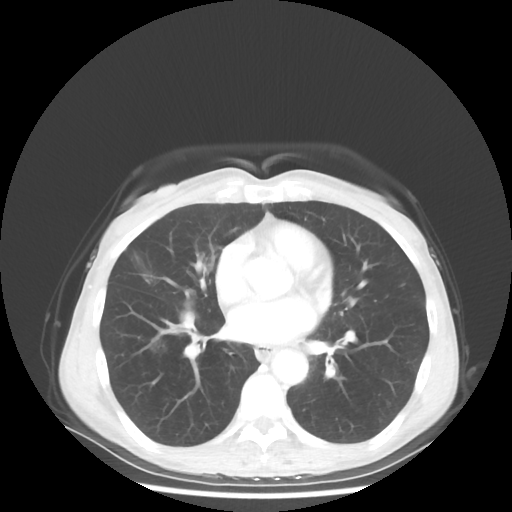
Chest CT, one axial slice. Position 25 of 56 along the scan axis. 80 kVp. Lung window (W 1500 / L -600 HU). 5 mm slice thickness. 512 × 512 image matrix. Female patient, age 57 years. From the clinical record (not read from this slice): clinical TNM (as recorded): T1c N3 M1a.
Structures marked on this image (bounding box drawn by a radiologist):
- lung tumour (recorded histology: adenocarcinoma): box from (x=180, y=311) to (x=192, y=328) px